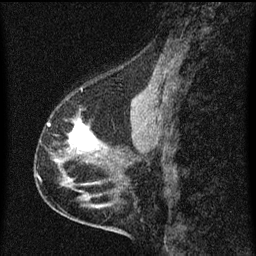
Breast MRI (dynamic contrast-enhanced), one sagittal slice. Position 28 of 60 along the scan axis. Dynamic contrast-enhanced series, image 2 of 3 at this slice position (ordered by acquisition). 1.5 T. TE 4.2 ms, TR 8 ms. 2 mm slice thickness. 256 × 256 image matrix, field of view 180 × 180 mm. Patient: female, 56 years.
Outlined on this slice (semi-automatic segmentation, software-assisted and operator-edited):
- analysis volume of interest (the breast-tissue region the enhancement analysis was run in; not a lesion): box from (x=35, y=116) to (x=102, y=181) px
- tumour enhancement mask (voxels above the 70 % enhancement threshold inside the analysis volume of interest): (x=69, y=122)–(x=96, y=150)